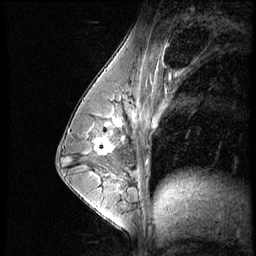
Breast MRI (dynamic contrast-enhanced), one sagittal slice; position 32 of 56 along the scan axis; dynamic contrast-enhanced series, image 2 of 4 at this slice position (ordered by acquisition); 1.5 T; TE 4.2 ms, TR 8.9 ms; 2.5 mm slice thickness; 256 × 256 image matrix, field of view 200 × 200 mm. Patient: female, 35 years. From the clinical record (not read from this slice): setting: breast cancer imaged before/during neoadjuvant chemotherapy; receptor status: HER2-positive.
Structures marked on this image (semi-automatic segmentation, software-assisted and operator-edited):
- analysis volume of interest (the breast-tissue region the enhancement analysis was run in; not a lesion): box from (x=73, y=111) to (x=131, y=164) px
- tumour enhancement mask (voxels above the 140 % enhancement threshold inside the analysis volume of interest): (x=94, y=118)–(x=125, y=154)